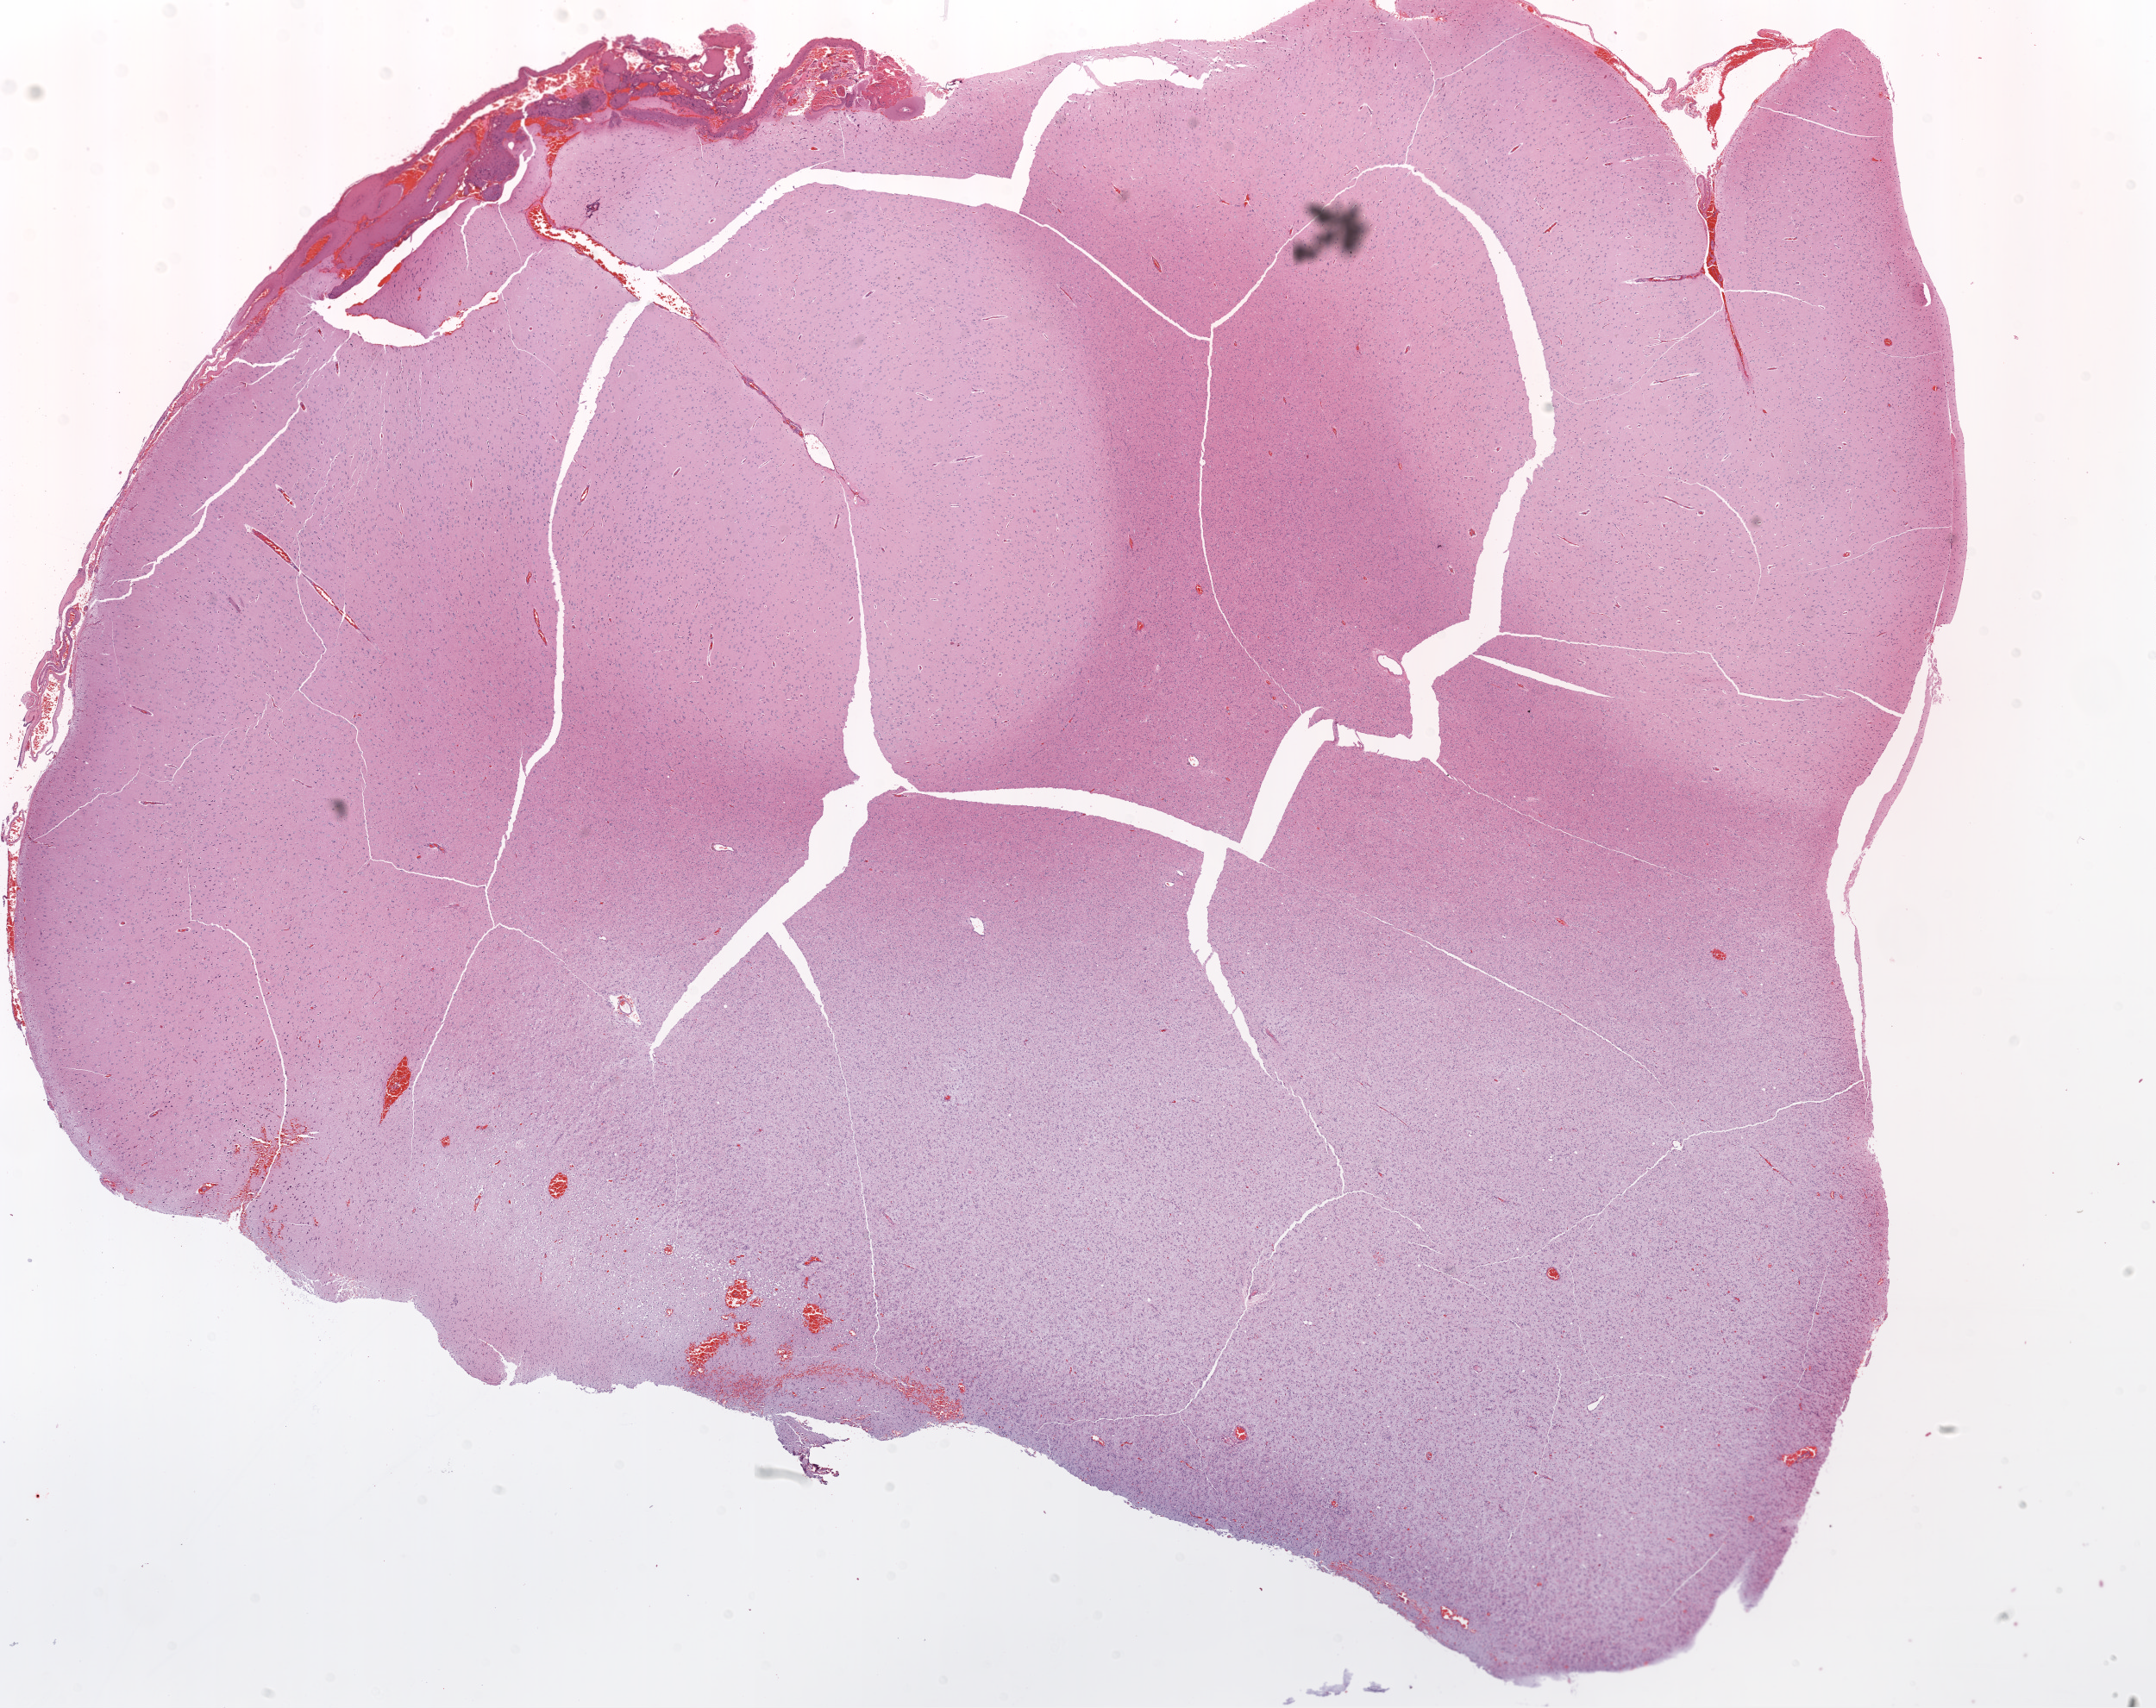
Digitized H&E-stained tissue section (whole slide) — low-resolution overview of the scanned area, about 20.1 x 15.9 mm (slide scanned at 20x), formalin-fixed paraffin-embedded (FFPE) diagnostic section, sample: primary tumour, brain. Male, age 71 years at initial diagnosis.
Pathologic diagnosis: Glioblastoma.